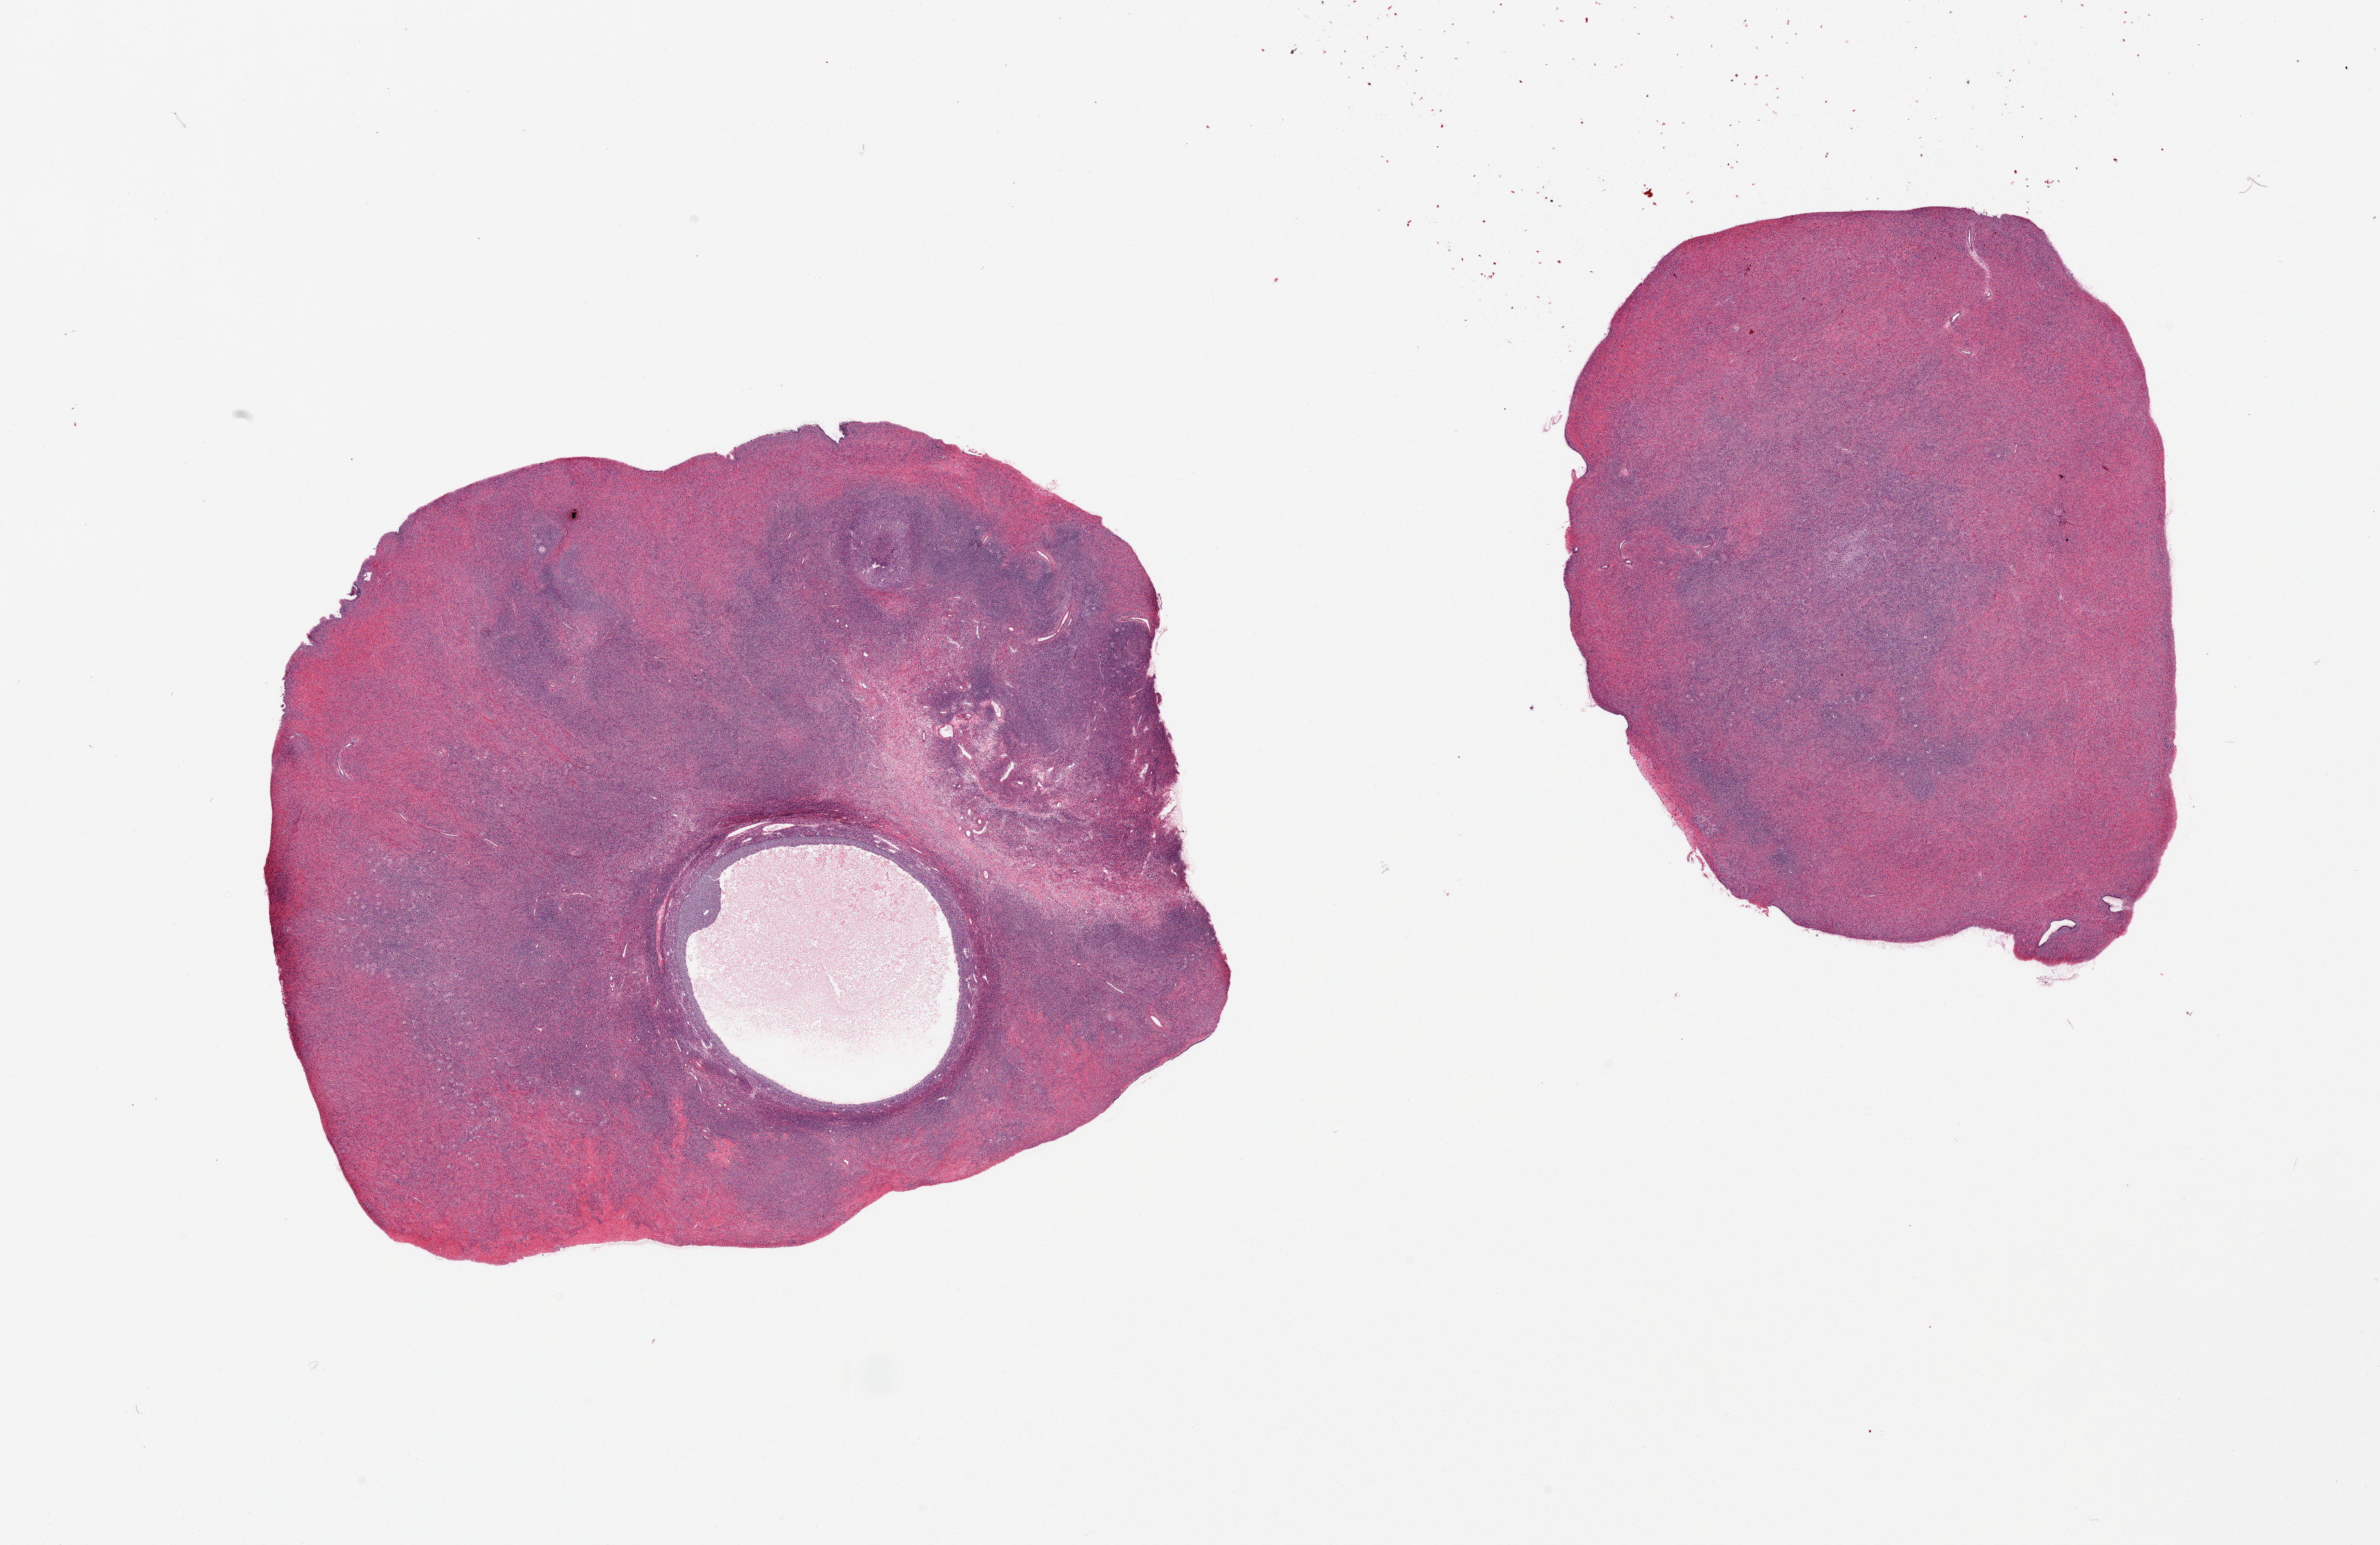
Hematoxylin and eosin (H&E) whole-slide image — a low-resolution overview of the entire scanned area, about 27.6 x 17.9 mm. PAXgene-fixed, paraffin-embedded tissue. Target tissue: ovary. Donor tissue sample. Donor sex: female.
Pathologist's review note for this sample: 2 pieces; Beautiful cumulus oophorus in one section.